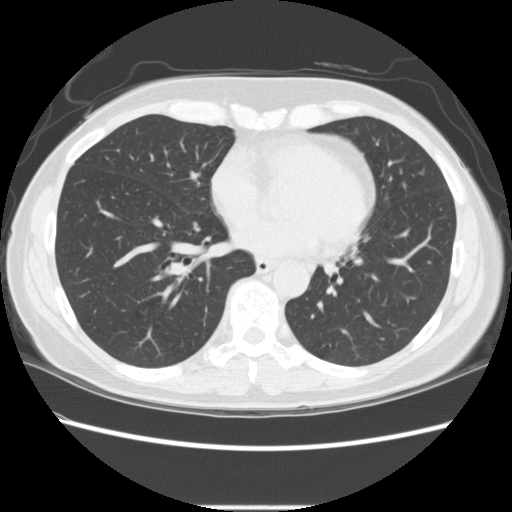
Low-dose screening chest CT, axial slice, baseline screening round, lung window (W 1500 / L -600 HU), 2.5 mm slice thickness, standard (soft-tissue) reconstruction kernel (STANDARD), 120 kVp, slice 147 of 256 in the series. Female participant, aged 60 years at enrolment. Current smoker at enrolment.
Lesion marked by an expert reader, box from (x=392, y=176) to (x=418, y=201) px. No non-calcified nodule or mass ≥4 mm was recorded by the screening reader at this exam.